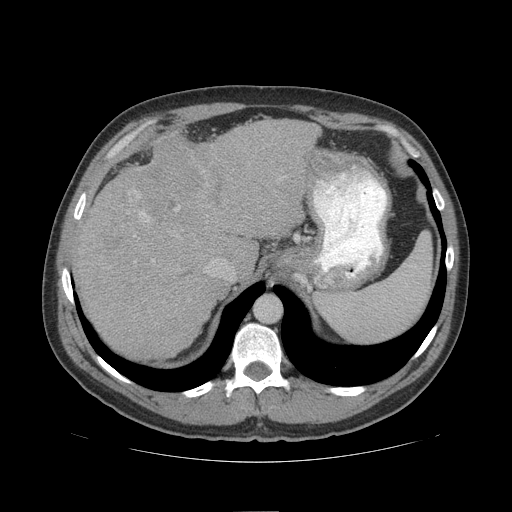
Contrast-enhanced abdominal CT (liver protocol), one axial slice; slice 78 of 109 in the series (ordered by position); reconstruction kernel STANDARD; soft-tissue window (W 400 / L 40 HU); 512 × 512 image matrix, field of view 420 × 420 mm. From the clinical record (not read from this slice): diagnosis: hepatocellular carcinoma (patient treated with transarterial chemoembolisation; whether this scan precedes or follows treatment is not stated here); TNM stage (as recorded): Stage-IIIB; Child-Pugh class: A; tumour differentiation: poorly differentiated; tumour nodularity: multinodular.
Outlined on this slice (semi-automatically segmented with operator editing):
- abdominal aorta: box from (x=256, y=295) to (x=281, y=322) px
- liver parenchyma outside the tumour (the mass and vessels are separate outlines, so this box may not span the whole liver): (x=72, y=120)–(x=318, y=358)
- mass: (x=106, y=129)–(x=209, y=230)